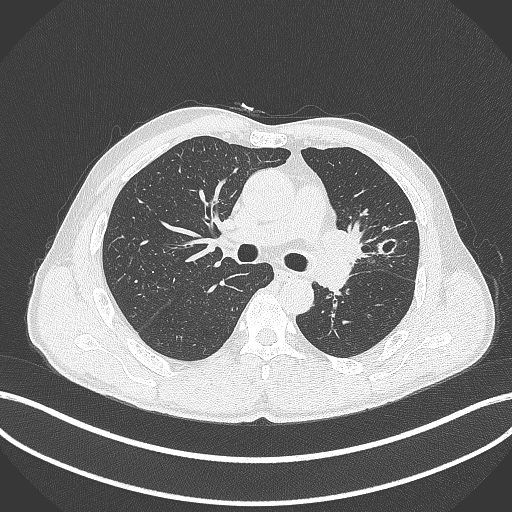
Chest CT, one axial slice; lung window (W 1500 / L -600 HU); 1 mm slice thickness; 512 × 512 image matrix, field of view 400 × 400 mm. Patient: male, 57 years. From the clinical record (not read from this slice): clinical TNM (as recorded): T2b N0 M0.
Outlined on this slice (bounding box drawn by a radiologist):
- lung tumour (recorded histology: squamous cell carcinoma): bounding box (x1, y1, x2, y2) in pixels: (316, 222, 369, 266)